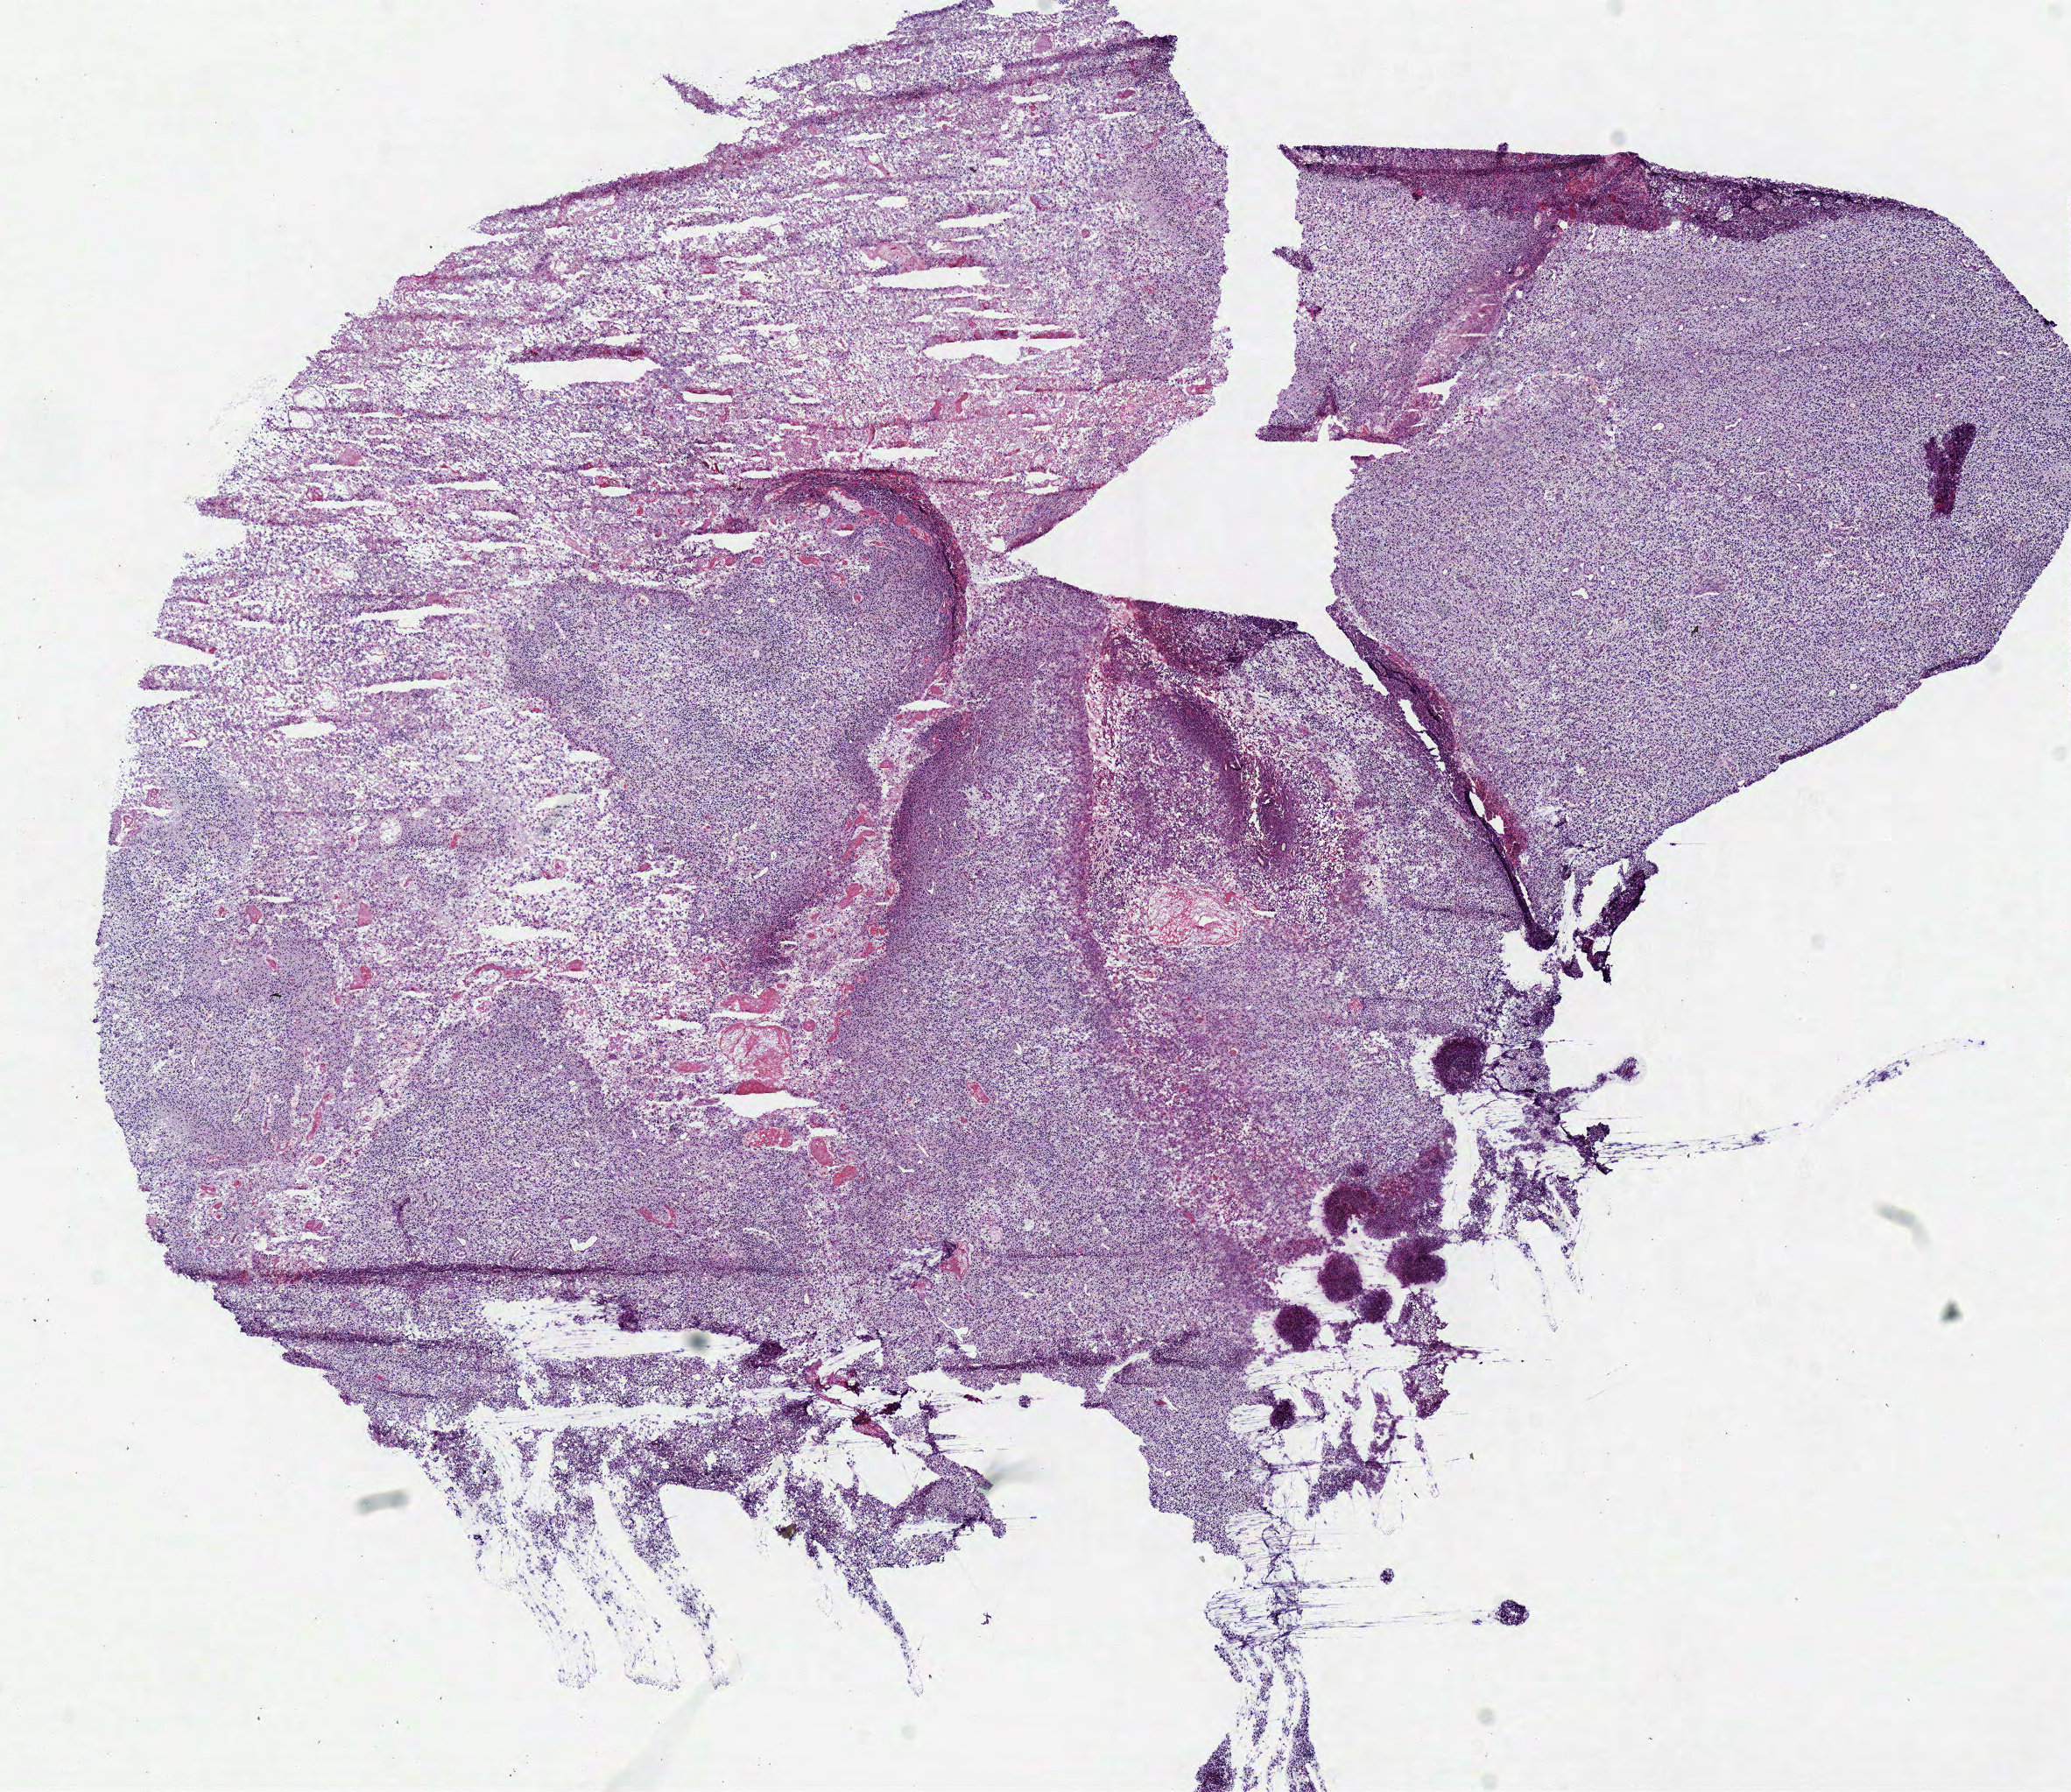
Digitized H&E-stained tissue section (whole slide), whole scanned area (about 9.3 x 8.0 mm) shown as a low-resolution overview; frozen section from the bottom of the tissue portion; sample: primary tumour, brain. Patient: female, age at initial diagnosis 58 years. Pathologist review of this section (percent, as recorded): tumour cells 90%, tumour nuclei 85%, normal cells 0%, stromal cells 0%, necrosis 10%.
Diagnosis: Glioblastoma.